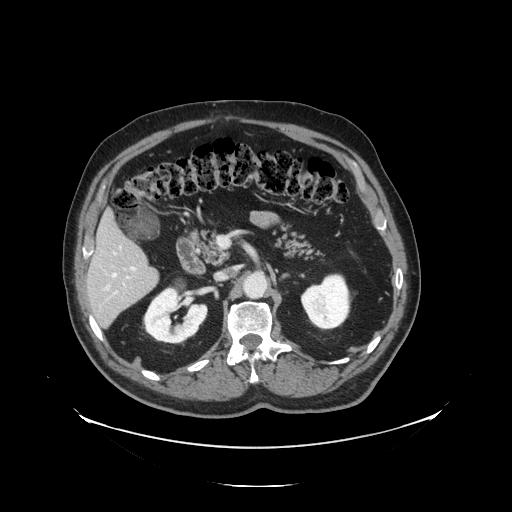
Contrast-enhanced abdominal CT, one axial slice. Position 67 of 138 along the scan axis. 120 kVp. Intravenous contrast given. Soft-tissue window (W 400 / L 40 HU). 2.5 mm slice thickness. 512 × 512 image matrix, field of view 497 × 497 mm. Male patient, age 77 years. Case-level facts recorded for this patient, not image findings: diagnosis: colorectal cancer liver metastases, imaged before liver resection.
Annotated regions visible in this slice (expert manual segmentation):
- liver: bounding box <89,215,158,328> (left, top, right, bottom; pixels)
- planned liver remnant (the part of the liver to remain after resection): <89,215,150,286>
- portal vein (with intrahepatic branches): <116,268,136,294>